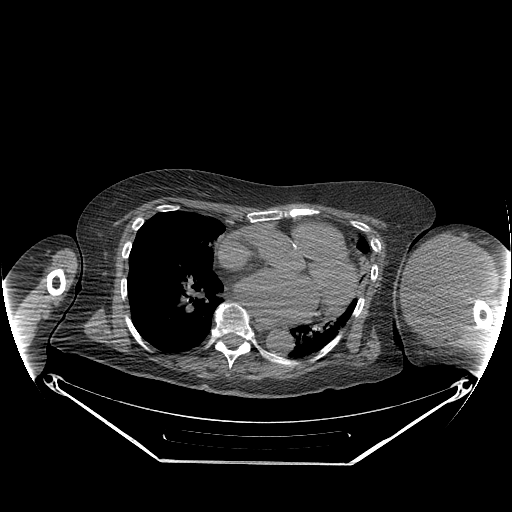
CT of an extremity soft-tissue mass (from a PET/CT study), one axial slice; position 165 of 267 along the scan axis; 140 kVp; soft-tissue window (W 400 / L 40 HU); 512 × 512 image matrix, field of view 500 × 500 mm. Female patient. From the clinical record (not read from this slice): histological type: pleiomorphic leiomyosarcoma; grade: high; site of the primary tumour: left biceps.
Annotated regions visible in this slice (expert contour drawn on MRI and transferred to this co-registered scan by the dataset authors):
- gross tumour volume including surrounding oedema: bounding box (x1, y1, x2, y2) in pixels: (402, 235, 490, 330)
- gross tumour volume (mass): (402, 235, 487, 328)